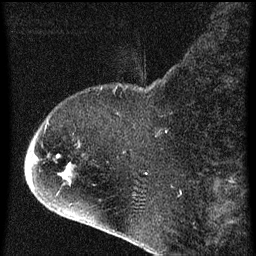
Breast MRI (dynamic contrast-enhanced), one sagittal slice; slice 16 of 60 in the series (ordered by position); dynamic contrast-enhanced series, image 2 of 4 at this slice position (ordered by acquisition); 1.5 T; TE 4.2 ms, TR 8 ms; 2 mm slice thickness; 256 × 256 image matrix. Patient: female, 71 years.
Annotated regions visible in this slice (semi-automatic segmentation, software-assisted and operator-edited):
- analysis volume of interest (the breast-tissue region the enhancement analysis was run in; not a lesion): bounding box (x1, y1, x2, y2) in pixels: (32, 86, 141, 205)
- tumour enhancement mask (voxels above the 70 % enhancement threshold inside the analysis volume of interest): (56, 154, 59, 159)